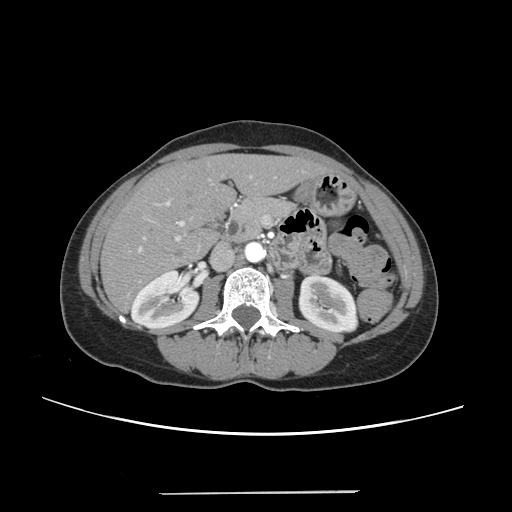
Contrast-enhanced abdominal CT, one axial slice. Position 111 of 240 along the scan axis. Intravenous contrast given. Soft-tissue window (W 400 / L 40 HU). 512 × 512 image matrix, field of view 371 × 371 mm. Female patient, age 60 years. From the clinical record (not read from this slice): diagnosis: colorectal cancer liver metastases, imaged before liver resection; multiple liver metastases: no; largest metastasis: 1.5 cm; disease in both lobes: no.
Structures marked on this image (manually delineated by an expert):
- liver: bounding box <103,156,323,309> (left, top, right, bottom; pixels)
- planned liver remnant (the part of the liver to remain after resection): <103,156,323,309>
- portal vein (with intrahepatic branches): <137,176,252,252>